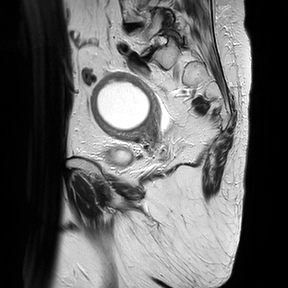
Pelvic MRI for cervical cancer, one sagittal slice; position 10 of 30 along the scan axis; T2-weighted; 1.5 T; TE 100 ms, TR 4816.3 ms; 4 mm slice thickness; 288 × 288 image matrix, field of view 300 × 300 mm. Patient: female, 74 years.
Structures marked on this image (manually delineated by an expert):
- uterus and cervix: box from (x=90, y=71) to (x=161, y=142) px